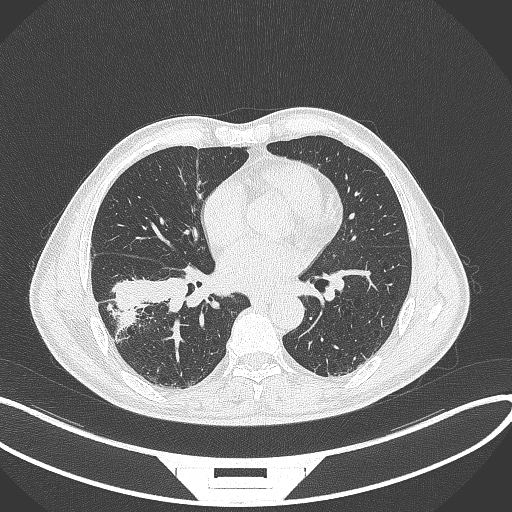
Chest CT, one axial slice. Position 163 of 364 along the scan axis. Reconstruction kernel B70f. 120 kVp. Lung window (W 1500 / L -600 HU). 512 × 512 image matrix, field of view 400 × 400 mm. Patient: male, 58 years. Case-level facts recorded for this patient, not image findings: clinical TNM (as recorded): T3 N0 M0; histopathological grade: G2.
Outlined on this slice (rectangle marked by the reading radiologist):
- lung tumour (recorded histology: squamous cell carcinoma): bounding box [x1, y1, x2, y2] px = [105, 282, 170, 325]